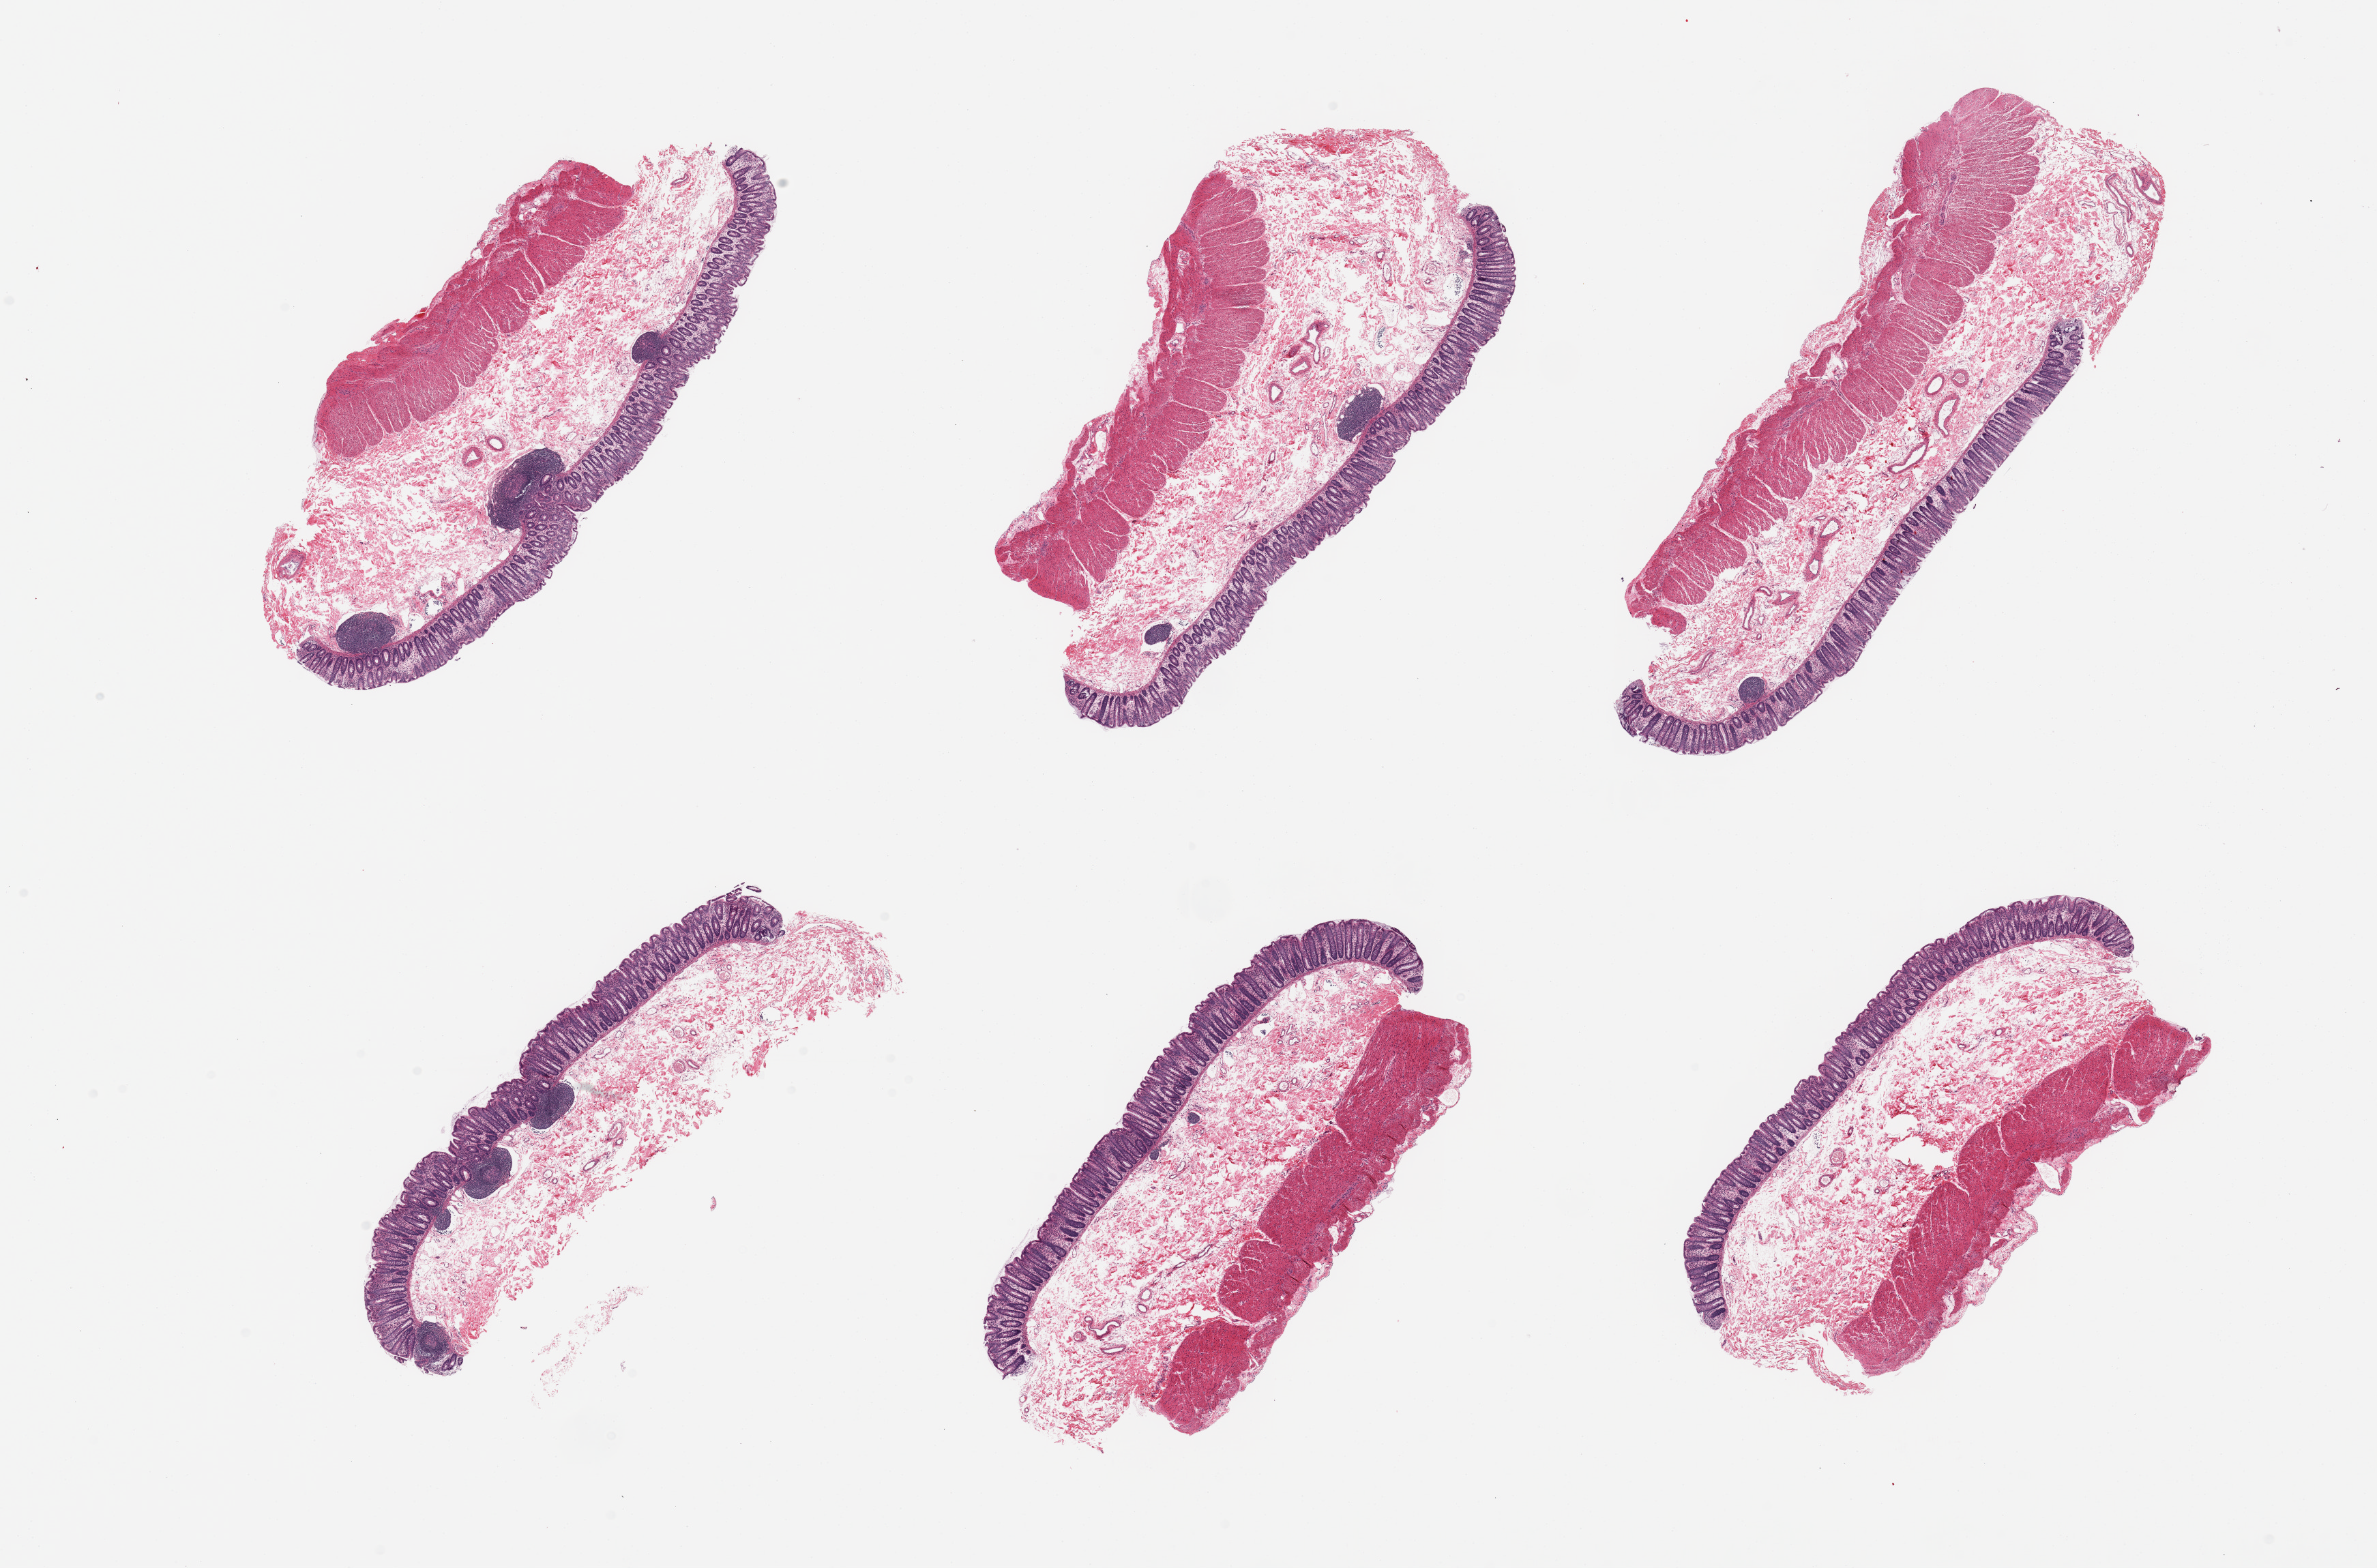
Hematoxylin and eosin (H&E) whole-slide image, brightfield — shown as a low-resolution overview of the whole scanned area (about 27.6 x 18.2 mm), PAXgene-fixed paraffin-embedded (PFPE) section, sampled site (target tissue): transverse colon, tissue donor sample. Male donor.
Reviewer comment on this tissue sample: 6 pieces; 5 are full thickness, 1 is without muscularis.